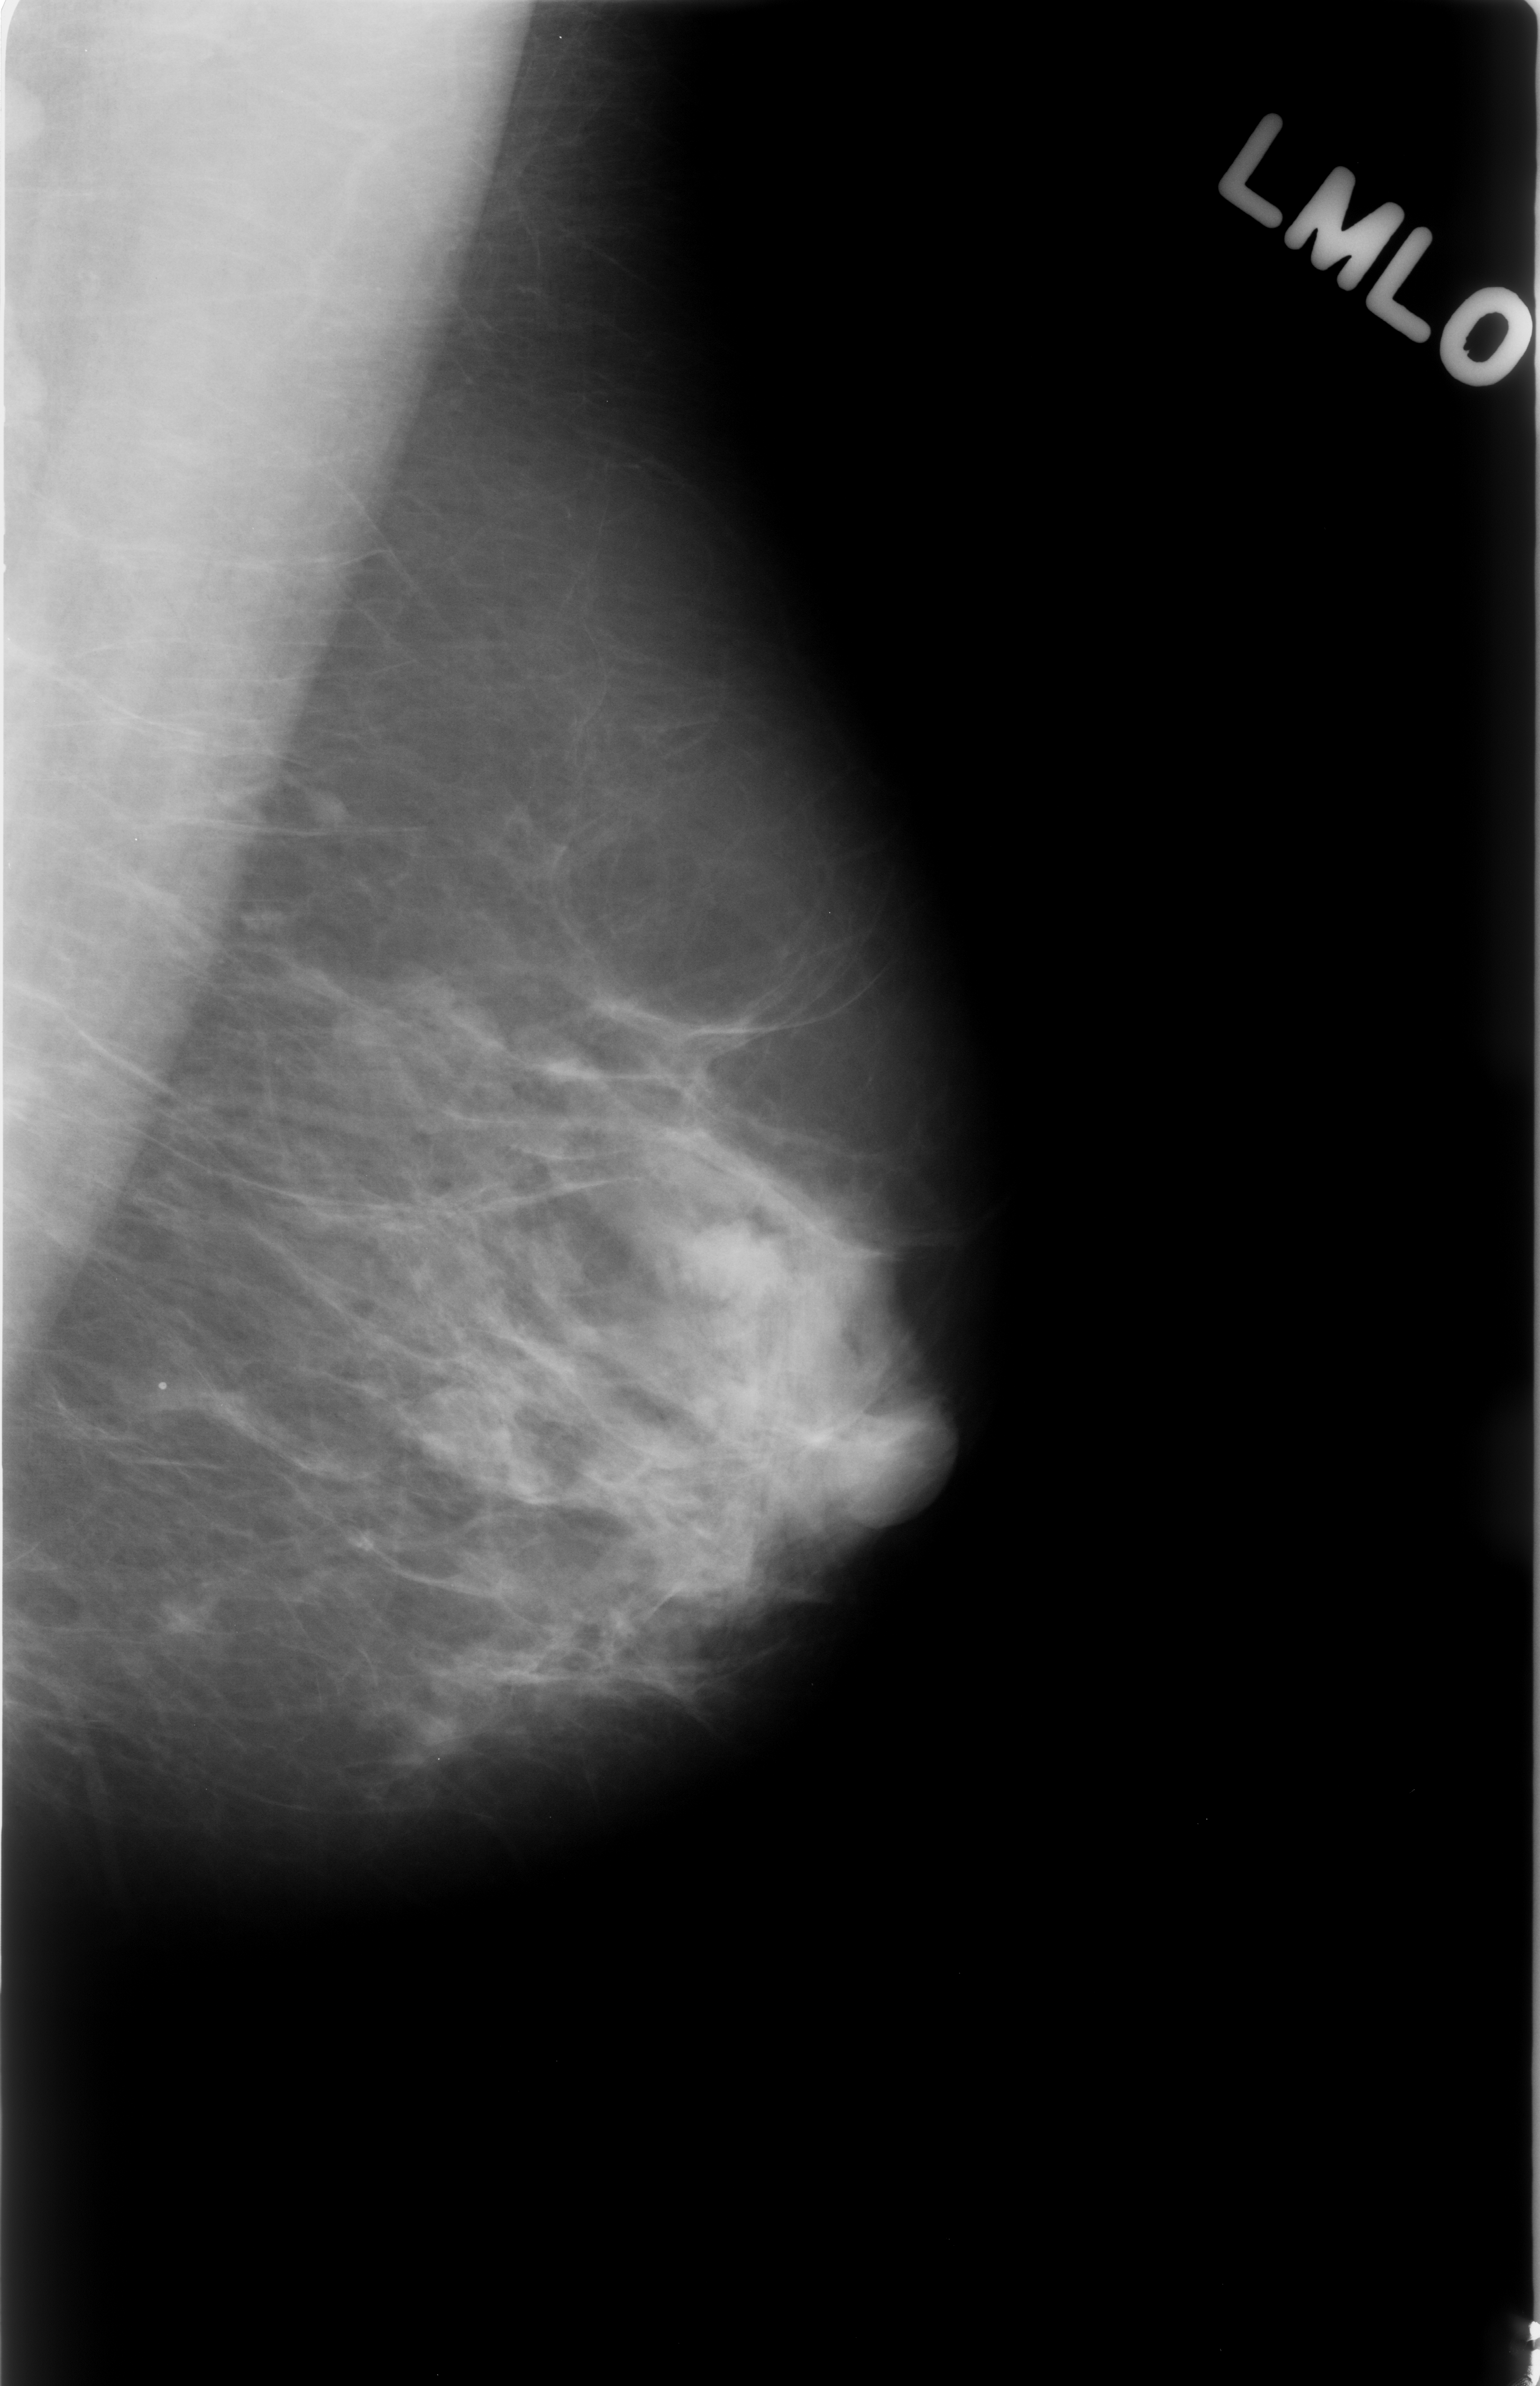
Scanned film-screen mammogram, left breast, mediolateral oblique (MLO) view, breast composition: scattered fibroglandular densities (BI-RADS density category 2 of 4).
- Radiologist-marked abnormalities on this image: mass, shape lobulated, margins circumscribed; BI-RADS assessment category 4; subtlety rating 5 on a 1 (subtle) to 5 (obvious) scale; pathology (as recorded): benign.